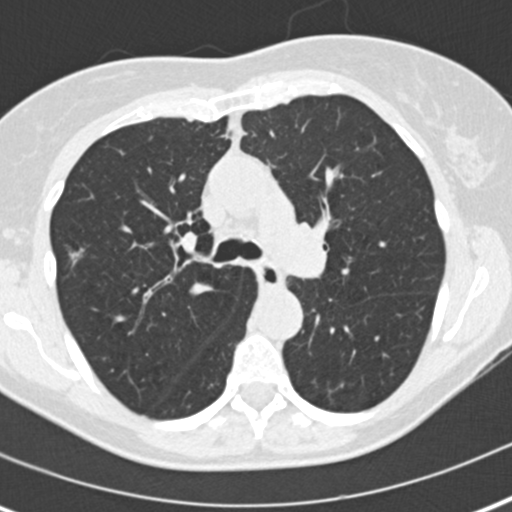
Low-dose screening chest CT, axial slice; second screening round (one year after baseline); lung window (W 1500 / L -600 HU); 2 mm slice thickness; 120 kVp; 512 × 512 image matrix. Female participant, aged 60 years at enrolment.
Expert-annotated lung lesion, bounding box (x1, y1, x2, y2) in pixels: (47, 228, 100, 277). Screening reader's record for this exam (one nodule recorded; not confirmed to be the boxed lesion): non-calcified nodule or mass ≥4 mm, right upper lobe, 8 × 6 mm, spiculated (stellate) margins, soft tissue attenuation, pre-existing on the prior screen: no. Participant outcome: lung cancer diagnosed 511 days after this screen (after the third annual screen) — bronchiolo-alveolar adenocarcinoma, NOS, right upper lobe, well differentiated (G1), stage IA (AJCC 6th edition), 11 mm at pathology.